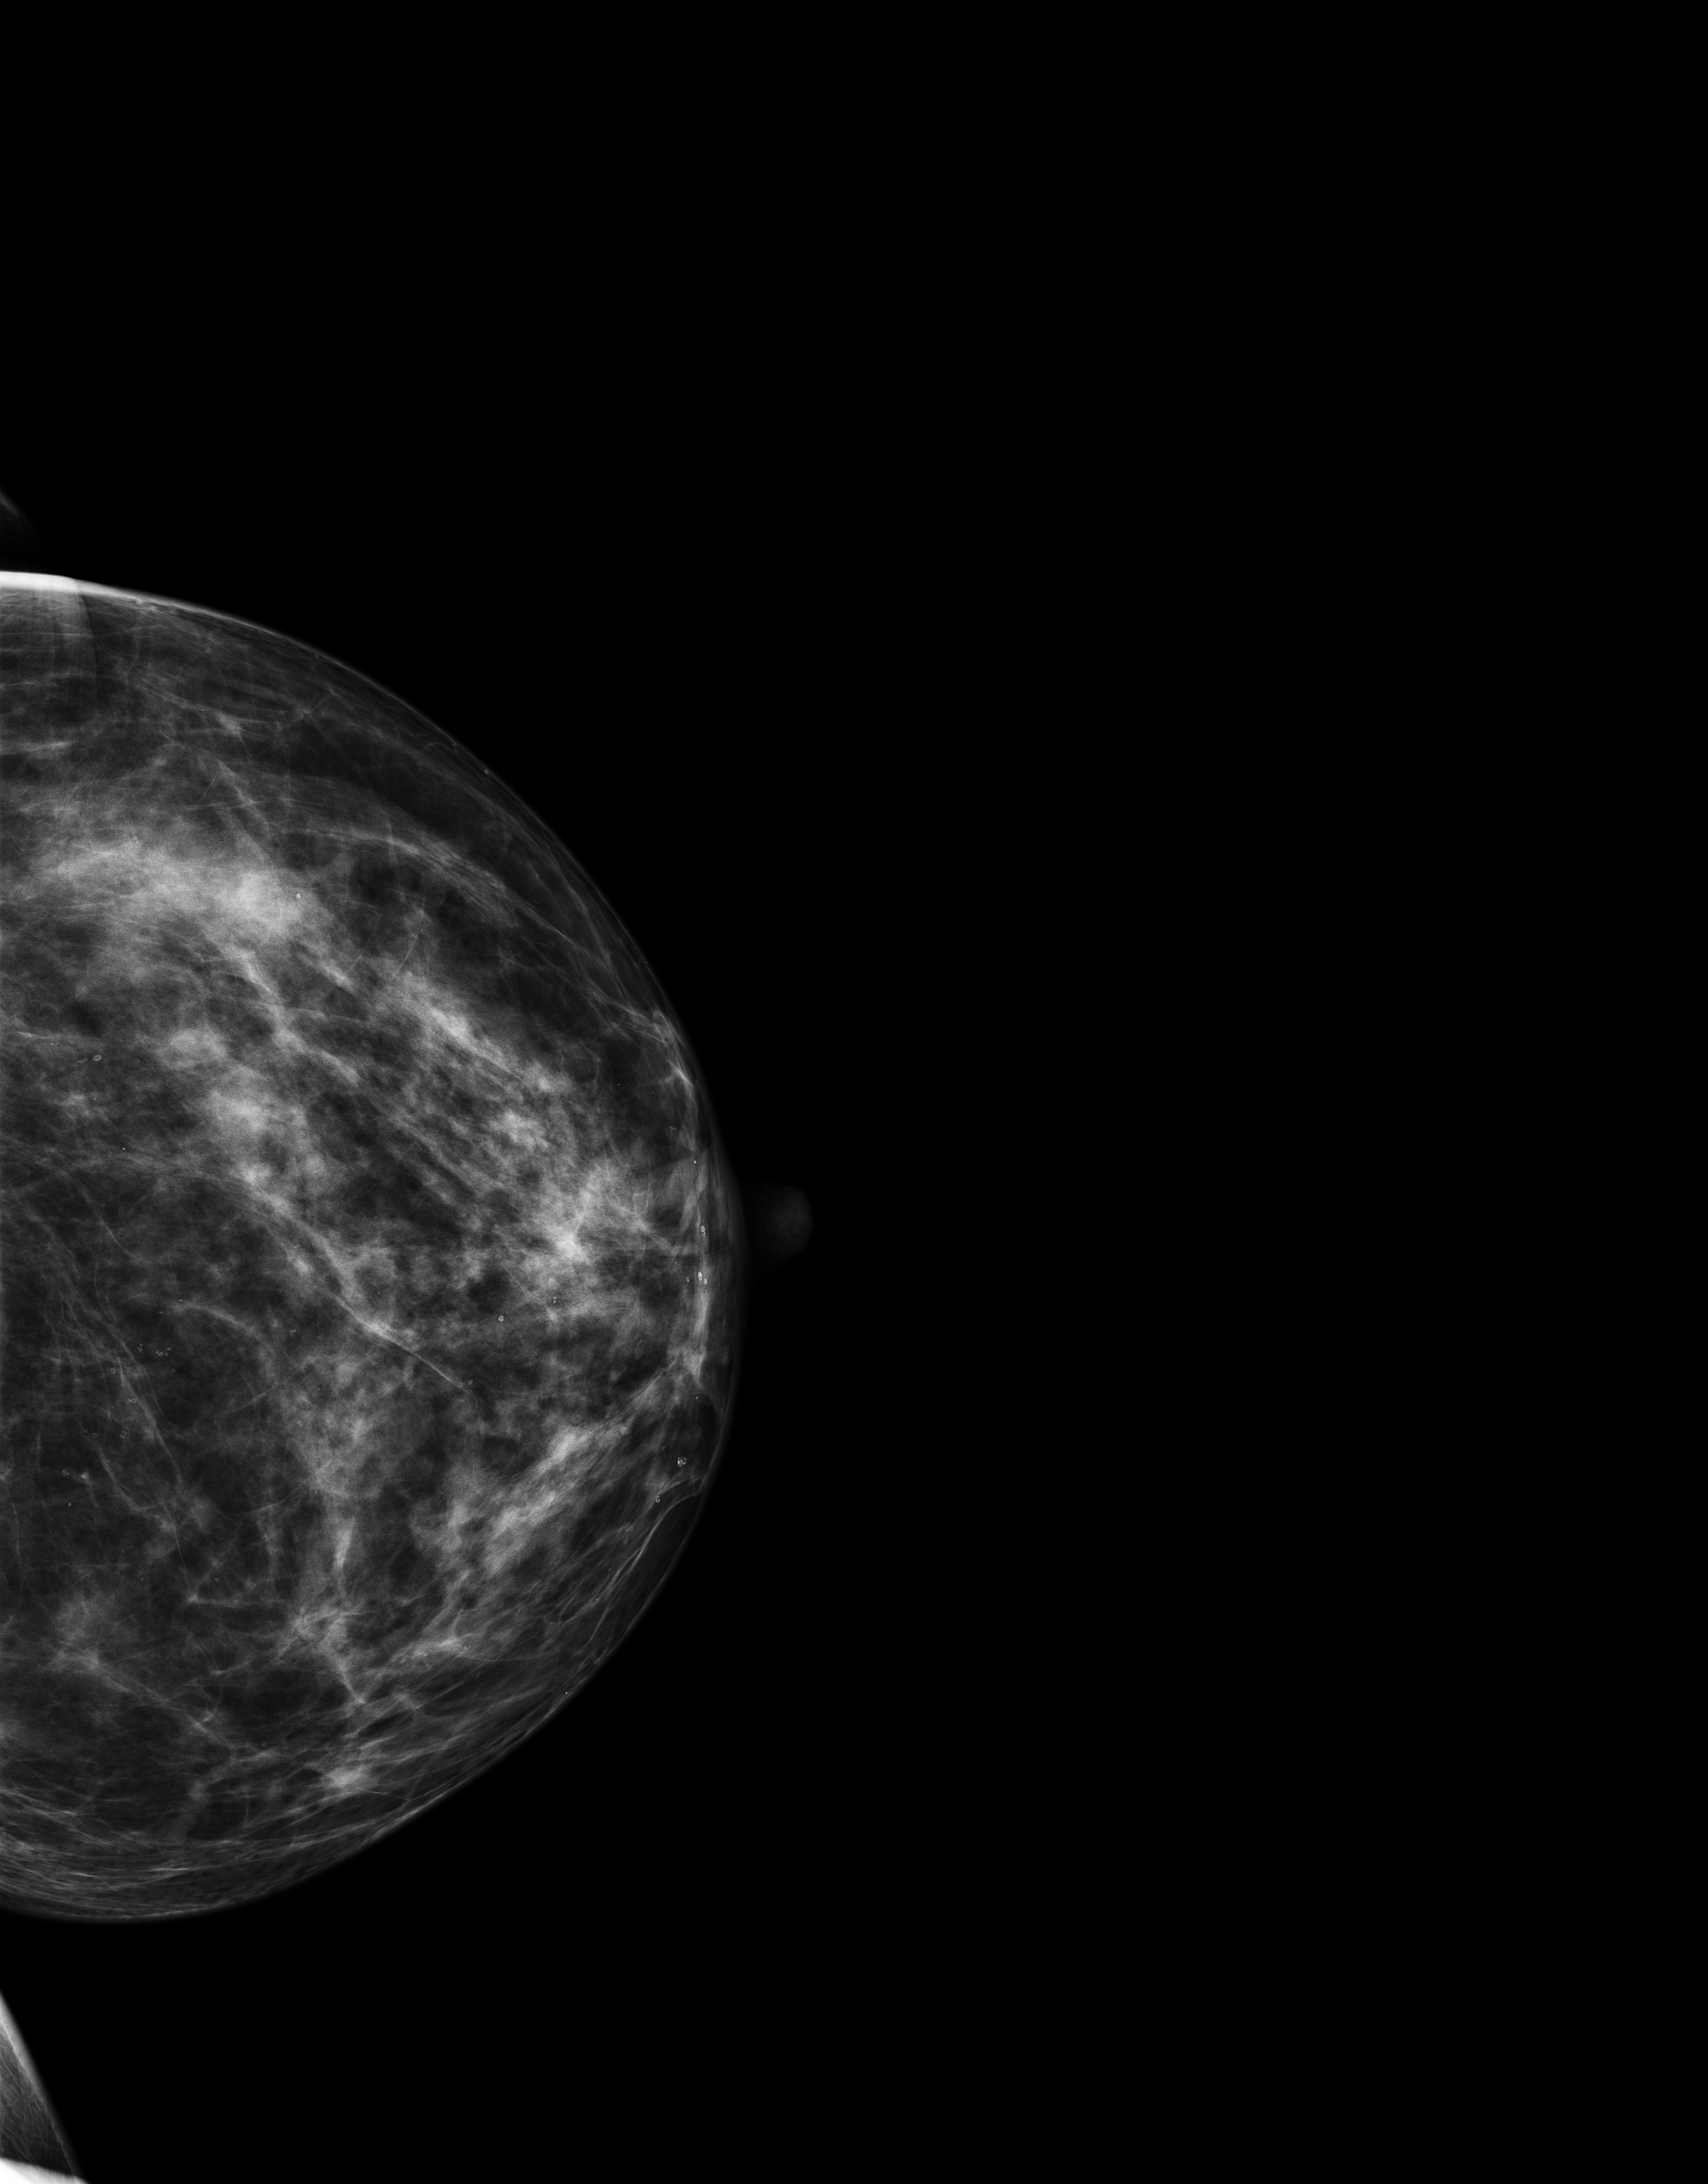
Full-field digital mammogram (FFDM); left breast; CC view; annual screening mammography examination; compressed breast thickness 65 mm; system: Senographe Essential ADS_56.21.3. Female patient, age 46 years.
Breast density at the screening exam (both breasts): heterogeneously dense (BI-RADS density category c). Final BI-RADS category for the screening round (tomosynthesis exam, both breasts): category 2. Recall: no recall after this screen.